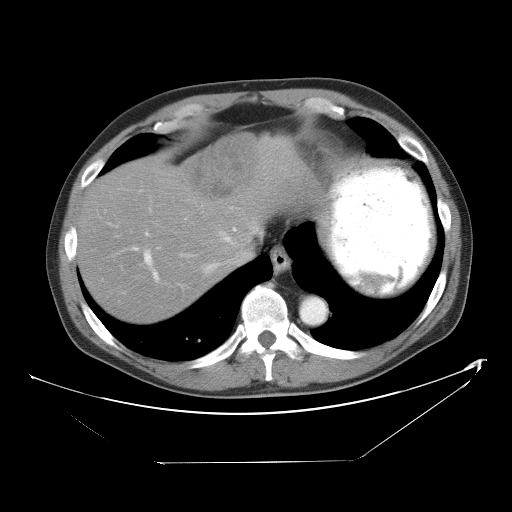
Contrast-enhanced abdominal CT, one axial slice. Reconstruction kernel STANDARD. 120 kVp. Soft-tissue window (W 400 / L 40 HU). 5 mm slice thickness. 512 × 512 image matrix. Male patient, age 59 years. From the clinical record (not read from this slice): diagnosis: colorectal cancer liver metastases, imaged before liver resection; multiple liver metastases: yes; largest metastasis: 8.5 cm; disease in both lobes: no.
Annotated regions visible in this slice (outlined manually by an expert reader):
- hepatic veins: box from (x=181, y=221) to (x=259, y=273) px
- liver: (x=79, y=134)–(x=320, y=322)
- planned liver remnant (the part of the liver to remain after resection): (x=79, y=168)–(x=228, y=322)
- portal vein (with intrahepatic branches): (x=144, y=208)–(x=236, y=280)
- liver metastasis: (x=190, y=135)–(x=253, y=200)